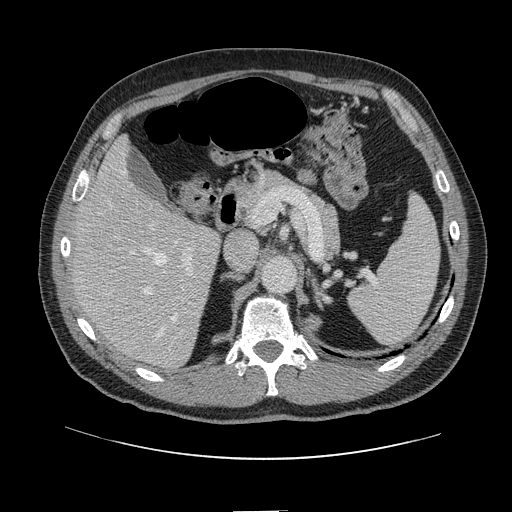
Contrast-enhanced abdominal CT, one axial slice; position 78 of 161 along the scan axis; 120 kVp; intravenous contrast given; soft-tissue window (W 400 / L 40 HU); 2.5 mm slice thickness; 512 × 512 image matrix, field of view 412 × 412 mm. Male patient, age 66 years. From the clinical record (not read from this slice): diagnosis: colorectal cancer liver metastases, imaged before liver resection; multiple liver metastases: no; largest metastasis: 3.5 cm; chemotherapy before resection: yes.
Annotated regions visible in this slice (expert manual segmentation):
- hepatic veins: bounding box <120,170,177,337> (left, top, right, bottom; pixels)
- liver: <75,140,219,368>
- planned liver remnant (the part of the liver to remain after resection): <75,140,200,297>
- portal vein (with intrahepatic branches): <119,222,196,314>